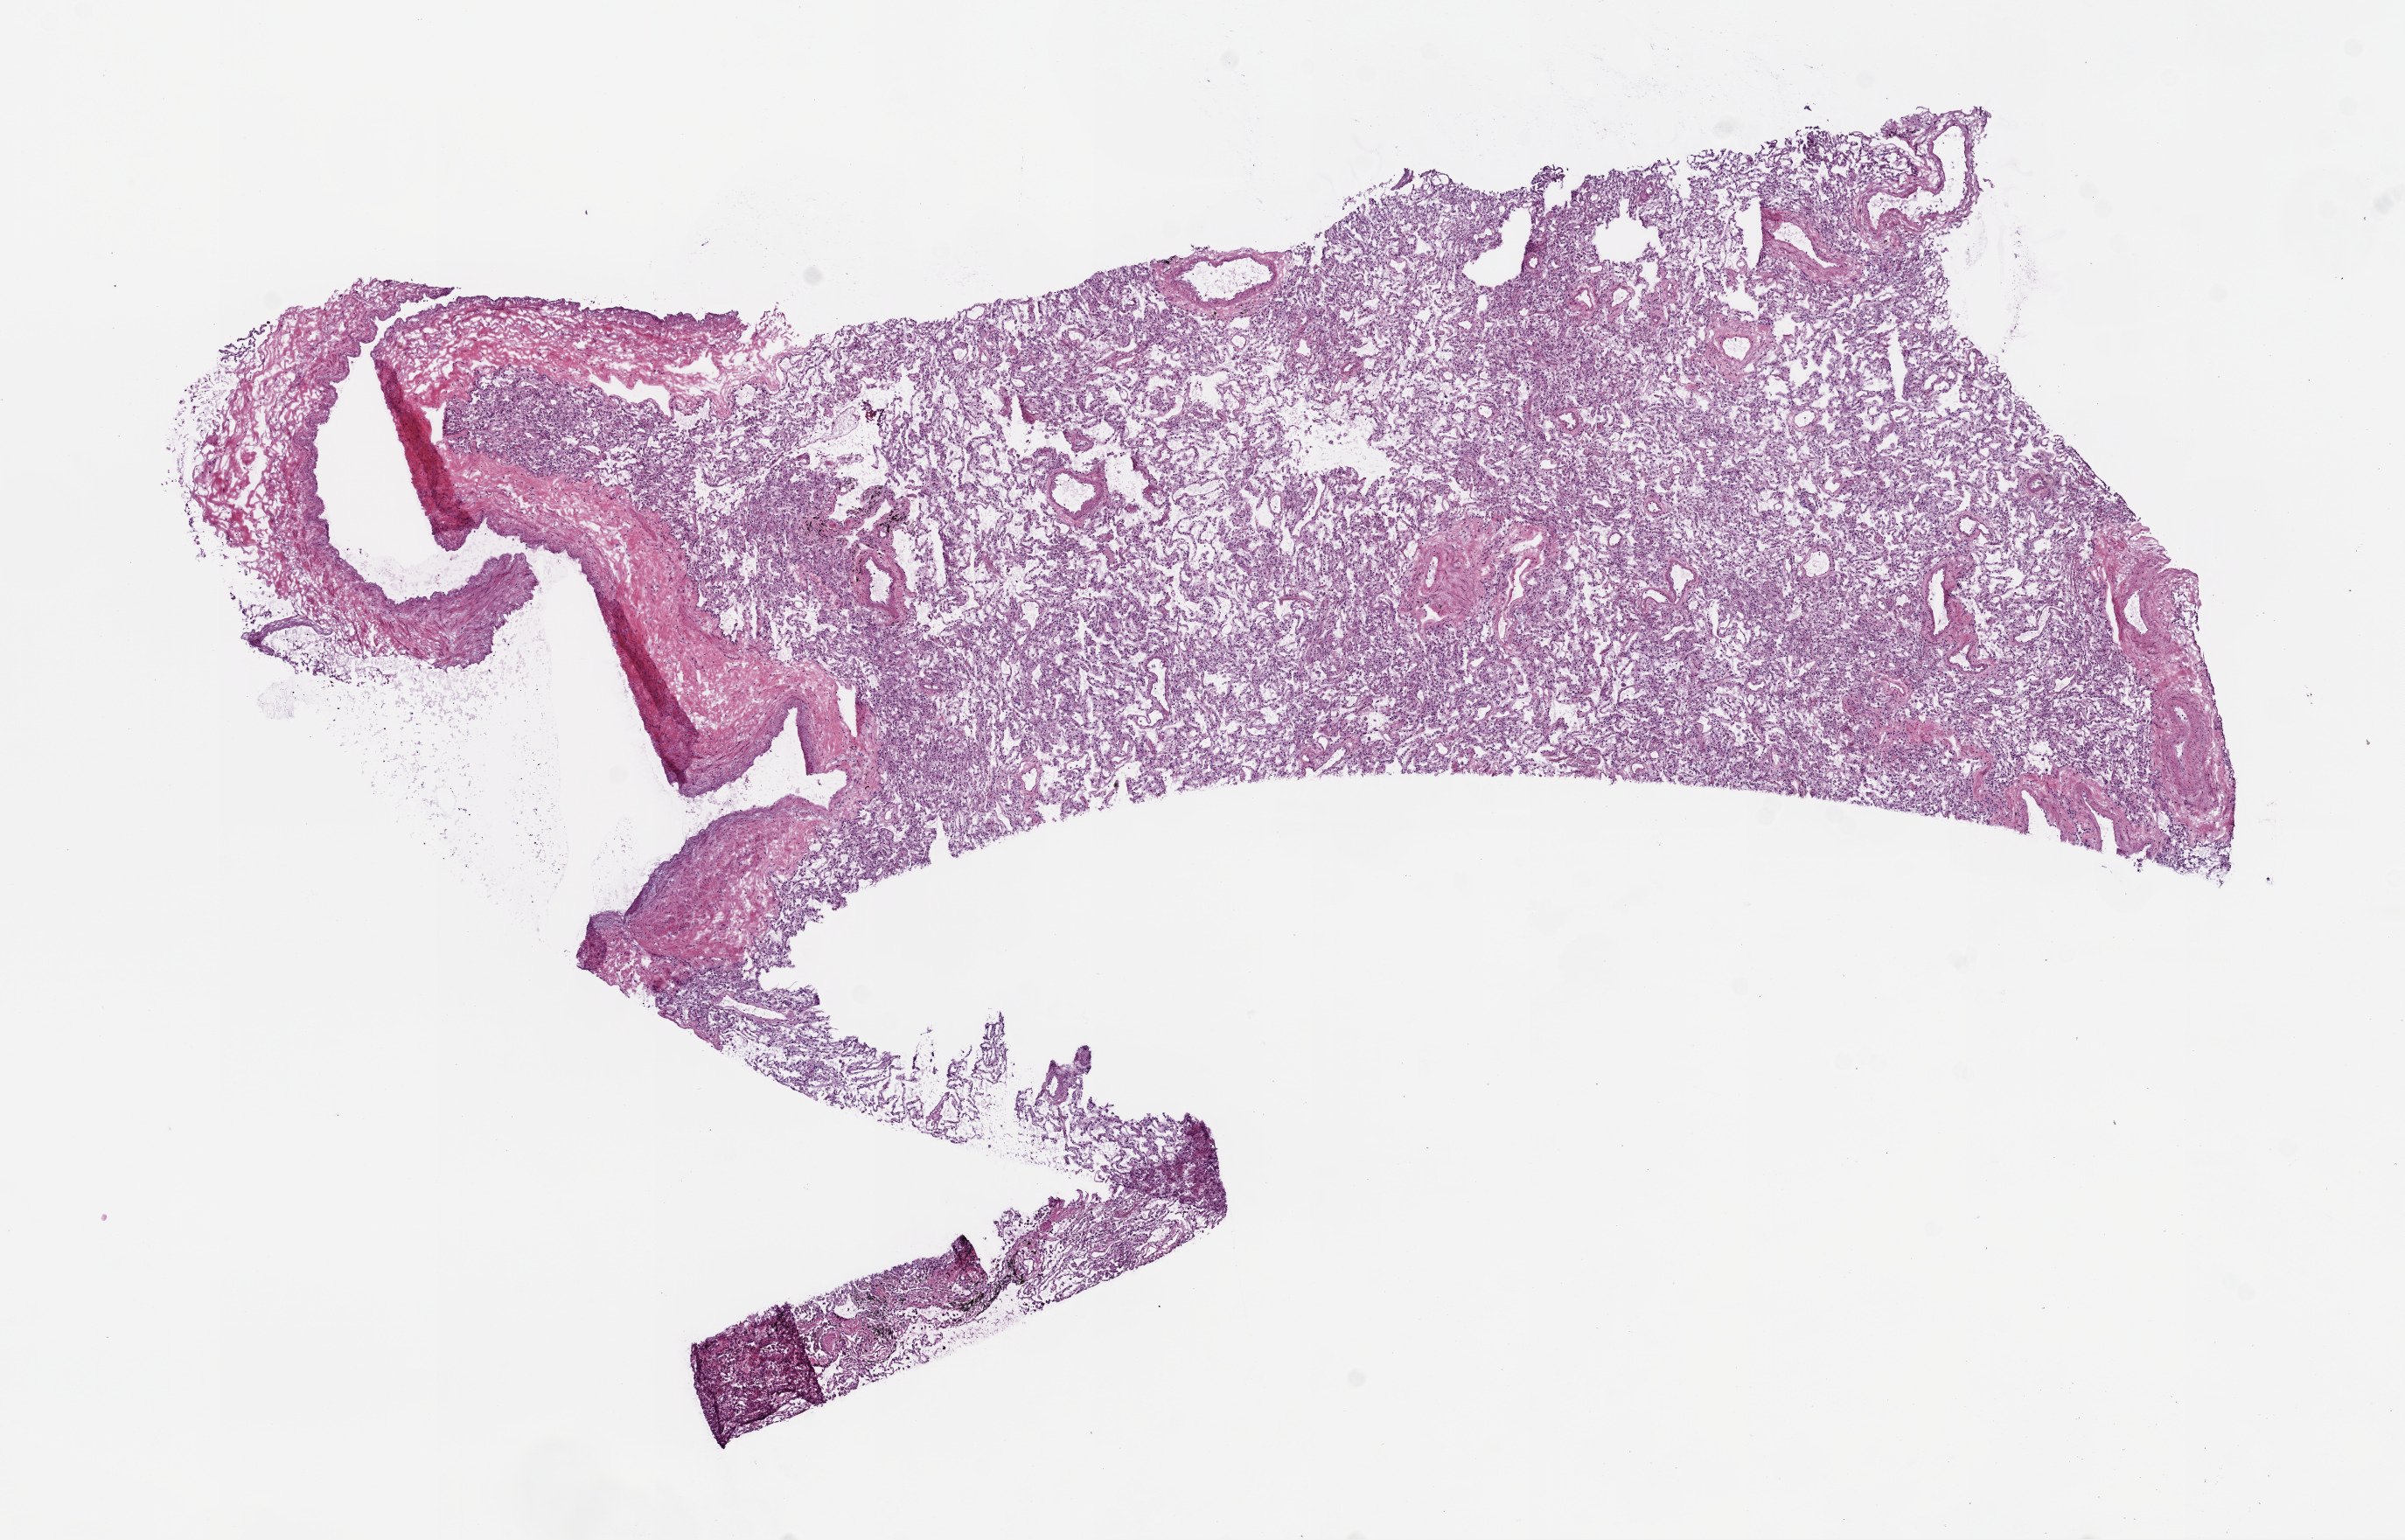
H&E whole-slide image, whole scanned area (about 11.0 x 7.1 mm, acquisition: 20x scan) shown as a low-resolution overview; frozen section; lung, solid tissue normal (non-tumour tissue) sample. Male, age 74 years at initial diagnosis.
This section: solid tissue normal sample (biorepository sample class). Patient diagnosis: Squamous cell carcinoma, NOS (lower lobe, lung).